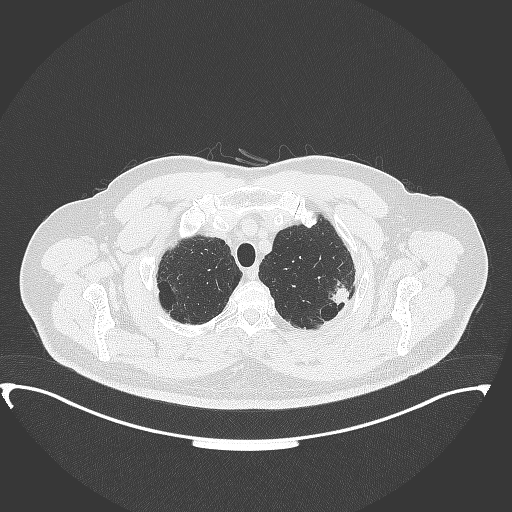
Chest CT, one axial slice. Slice 318 of 350 in the series (ordered by position). 120 kVp. Lung window (W 1500 / L -600 HU). 1 mm slice thickness. 512 × 512 image matrix. Male patient, age 64 years. Case-level facts recorded for this patient, not image findings: clinical TNM (as recorded): T1c N1 M1.
Structures marked on this image (rectangle marked by the reading radiologist):
- lung tumour (recorded histology: adenocarcinoma): bounding box [x1, y1, x2, y2] px = [330, 281, 353, 308]